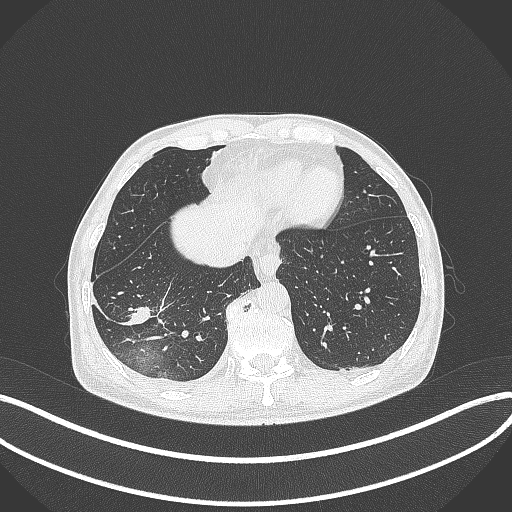
Chest CT, one axial slice. Position 91 of 388 along the scan axis. 120 kVp. Lung window (W 1500 / L -600 HU). 512 × 512 image matrix. Patient: male, 64 years. From the clinical record (not read from this slice): clinical TNM (as recorded): T3 N0 M0; histopathological grade: G2-3.
Annotated regions visible in this slice (bounding box drawn by a radiologist):
- lung tumour (recorded histology: adenocarcinoma): bounding box [x1, y1, x2, y2] px = [123, 304, 150, 327]